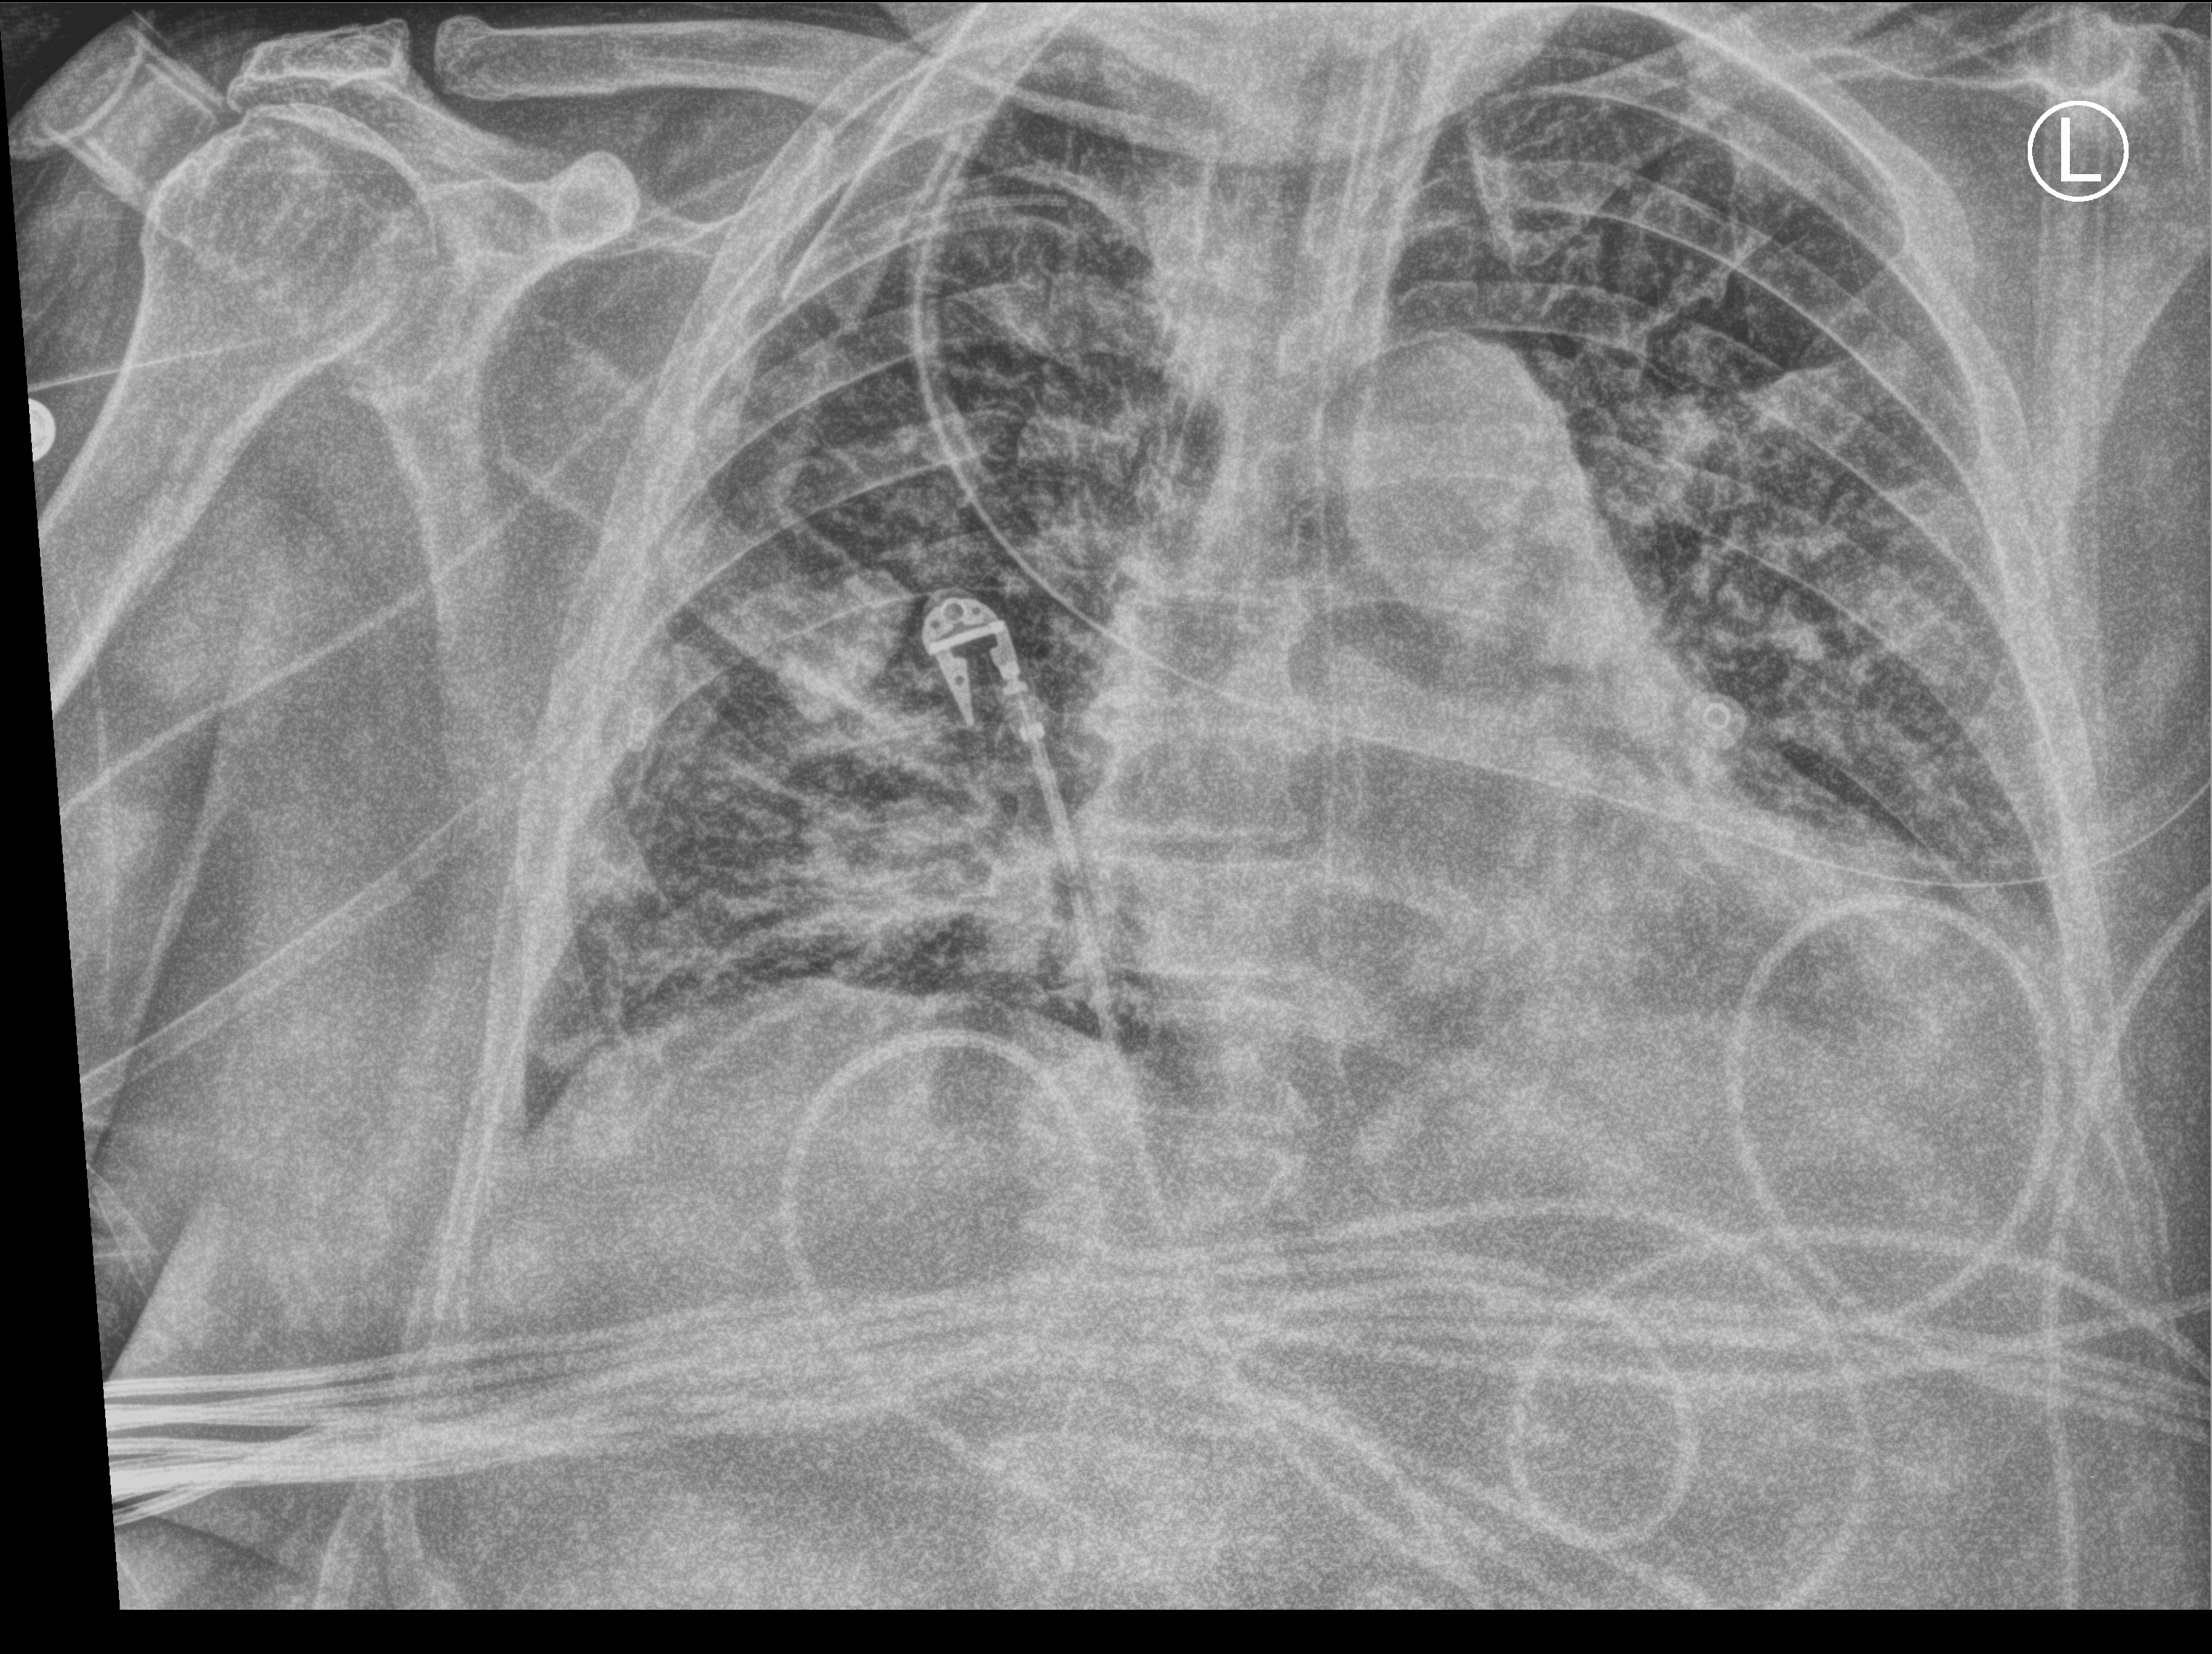
Portable chest radiograph, anteroposterior (AP) projection. Male patient hospitalised with COVID-19, age 60–74 years.
From the hospital-stay record, not from the radiograph (when in the stay this image was taken is not recorded): admitted to intensive care during this hospital stay: yes.